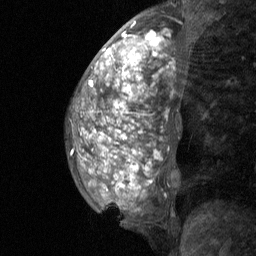
Breast MRI (dynamic contrast-enhanced), one sagittal slice. Position 24 of 64 along the scan axis. Dynamic contrast-enhanced study with each time point stored as its own series, time point 2 of 3 at this slice position (early post-contrast, ordered by acquisition time). 1.5 T. TE 4.8 ms, TR 27 ms. 2 mm slice thickness. 256 × 256 image matrix. Patient: female, 36 years. From the clinical record (not read from this slice): setting: breast cancer imaged before/during neoadjuvant chemotherapy; receptor status: HR-positive, HER2-negative.
Annotated regions visible in this slice (semi-automatic segmentation, software-assisted and operator-edited):
- analysis volume of interest (the breast-tissue region the enhancement analysis was run in; not a lesion): bounding box [x1, y1, x2, y2] px = [67, 12, 194, 230]
- tumour enhancement mask (voxels above the 90 % enhancement threshold inside the analysis volume of interest): [89, 22, 165, 190]